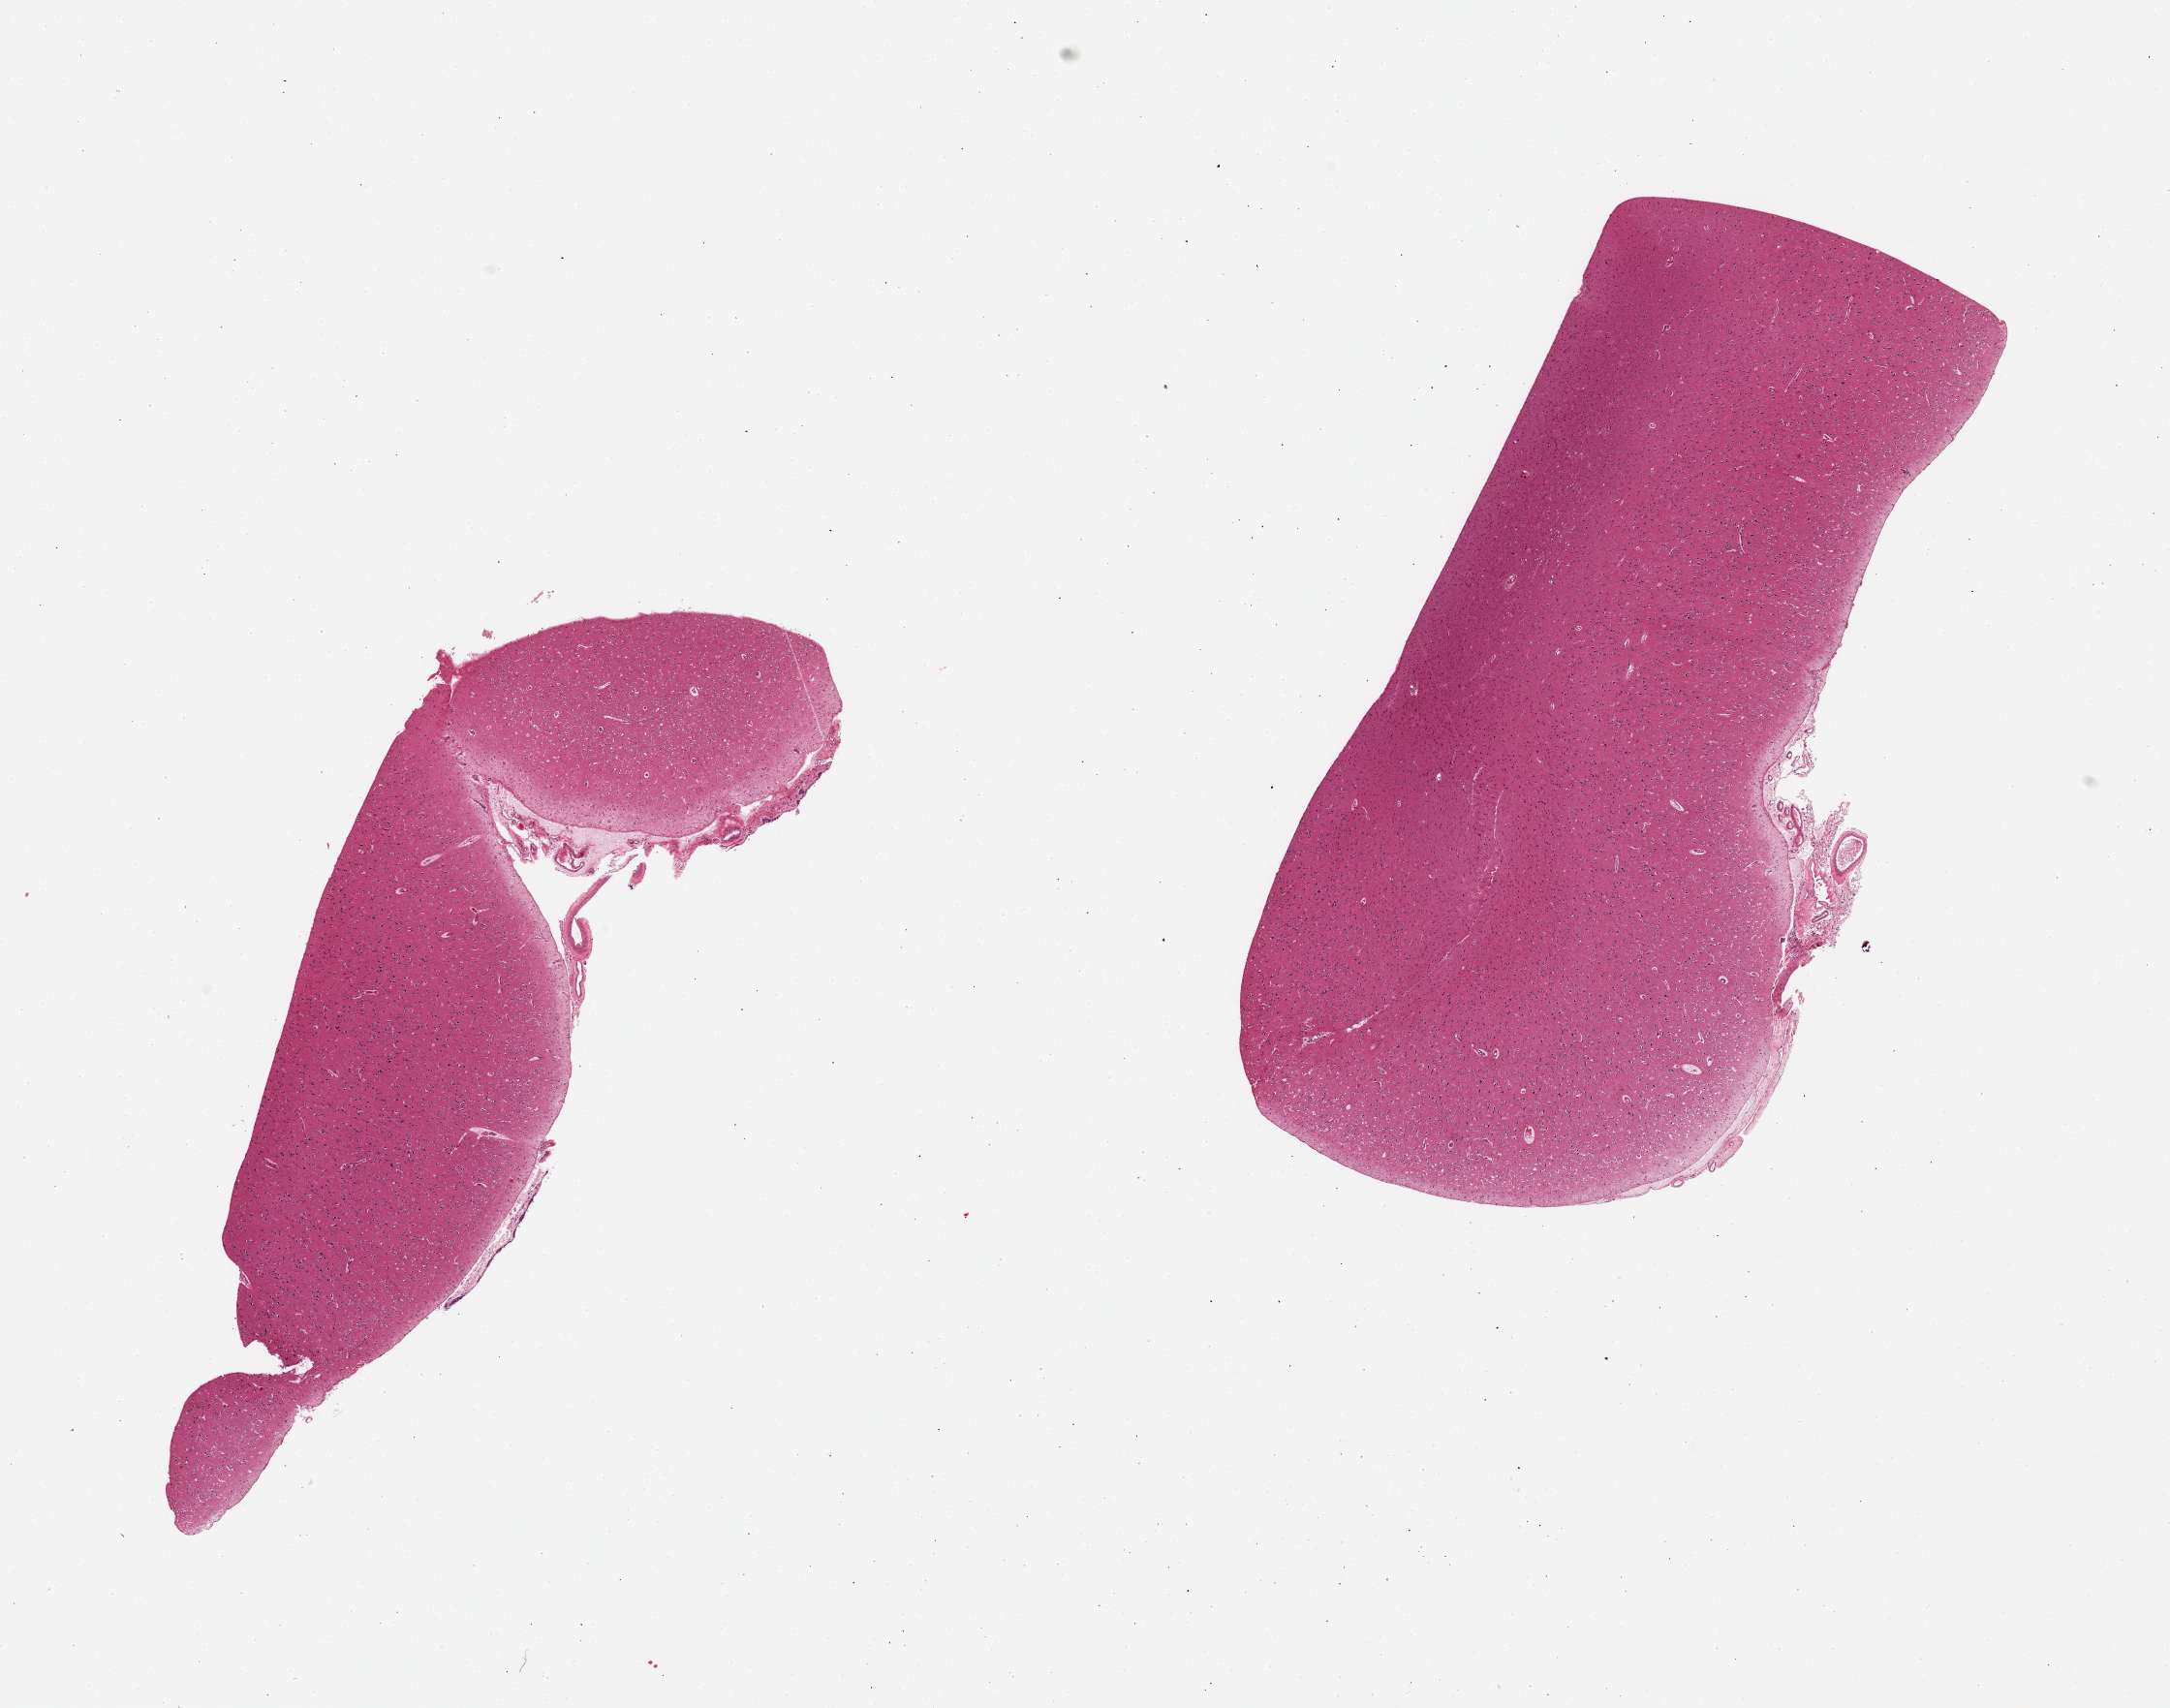
Hematoxylin and eosin (H&E) whole-slide image — low-resolution overview of the scanned area, about 17.7 x 13.9 mm; PAXgene-fixed paraffin-embedded (PFPE) section; sampled site (target tissue): cerebral cortex; tissue donor sample. Donor sex: male.
Review note (as recorded): 2 pieces, no abnormalities.